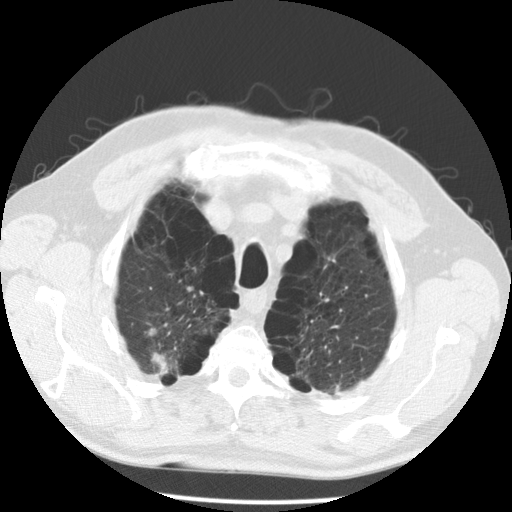
Low-dose screening chest CT, axial slice, second screening round (one year after baseline), lung window (W 1500 / L -600 HU), 2.5 mm slice thickness, slice 28 of 167 in the series. Male participant, aged 68 years at enrolment.
- Expert reader's lesion annotation, bounding box [x1, y1, x2, y2] px = [123, 312, 197, 388].
- The screening reader recorded 2 non-calcified nodules or masses ≥4 mm on this exam (lingula, left lower lobe); which of them this box marks is not recorded.
- Official screen result: positive, no significant change: stable abnormalities potentially related to lung cancer, unchanged since the prior screening exam.
- Later outcome: lung cancer diagnosed 617 days after this screen (after the third annual screen) — large cell carcinoma, NOS, right upper lobe, poorly differentiated (G3), stage IV (AJCC 6th edition).